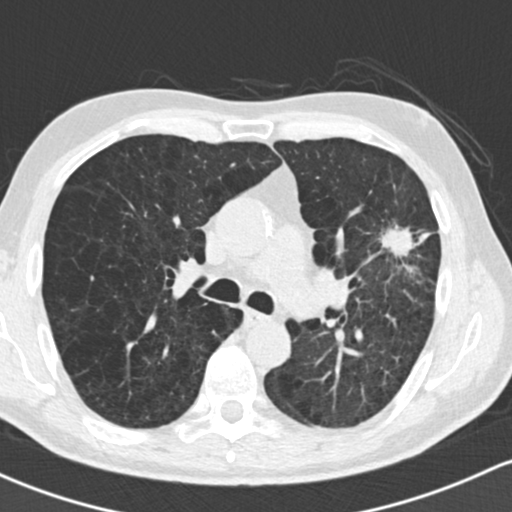
Low-dose screening chest CT, one axial slice. Position 96 of 162 along the scan axis. Reconstruction kernel B30f. 120 kVp. Lung window (W 1500 / L -600 HU). 2 mm slice thickness. 512 × 512 image matrix, field of view 318 × 318 mm.
Annotated regions visible in this slice (expert manual segmentation):
- lesion 1 (tumor, upper lobe of left lung): bounding box [x1, y1, x2, y2] px = [380, 226, 418, 258]